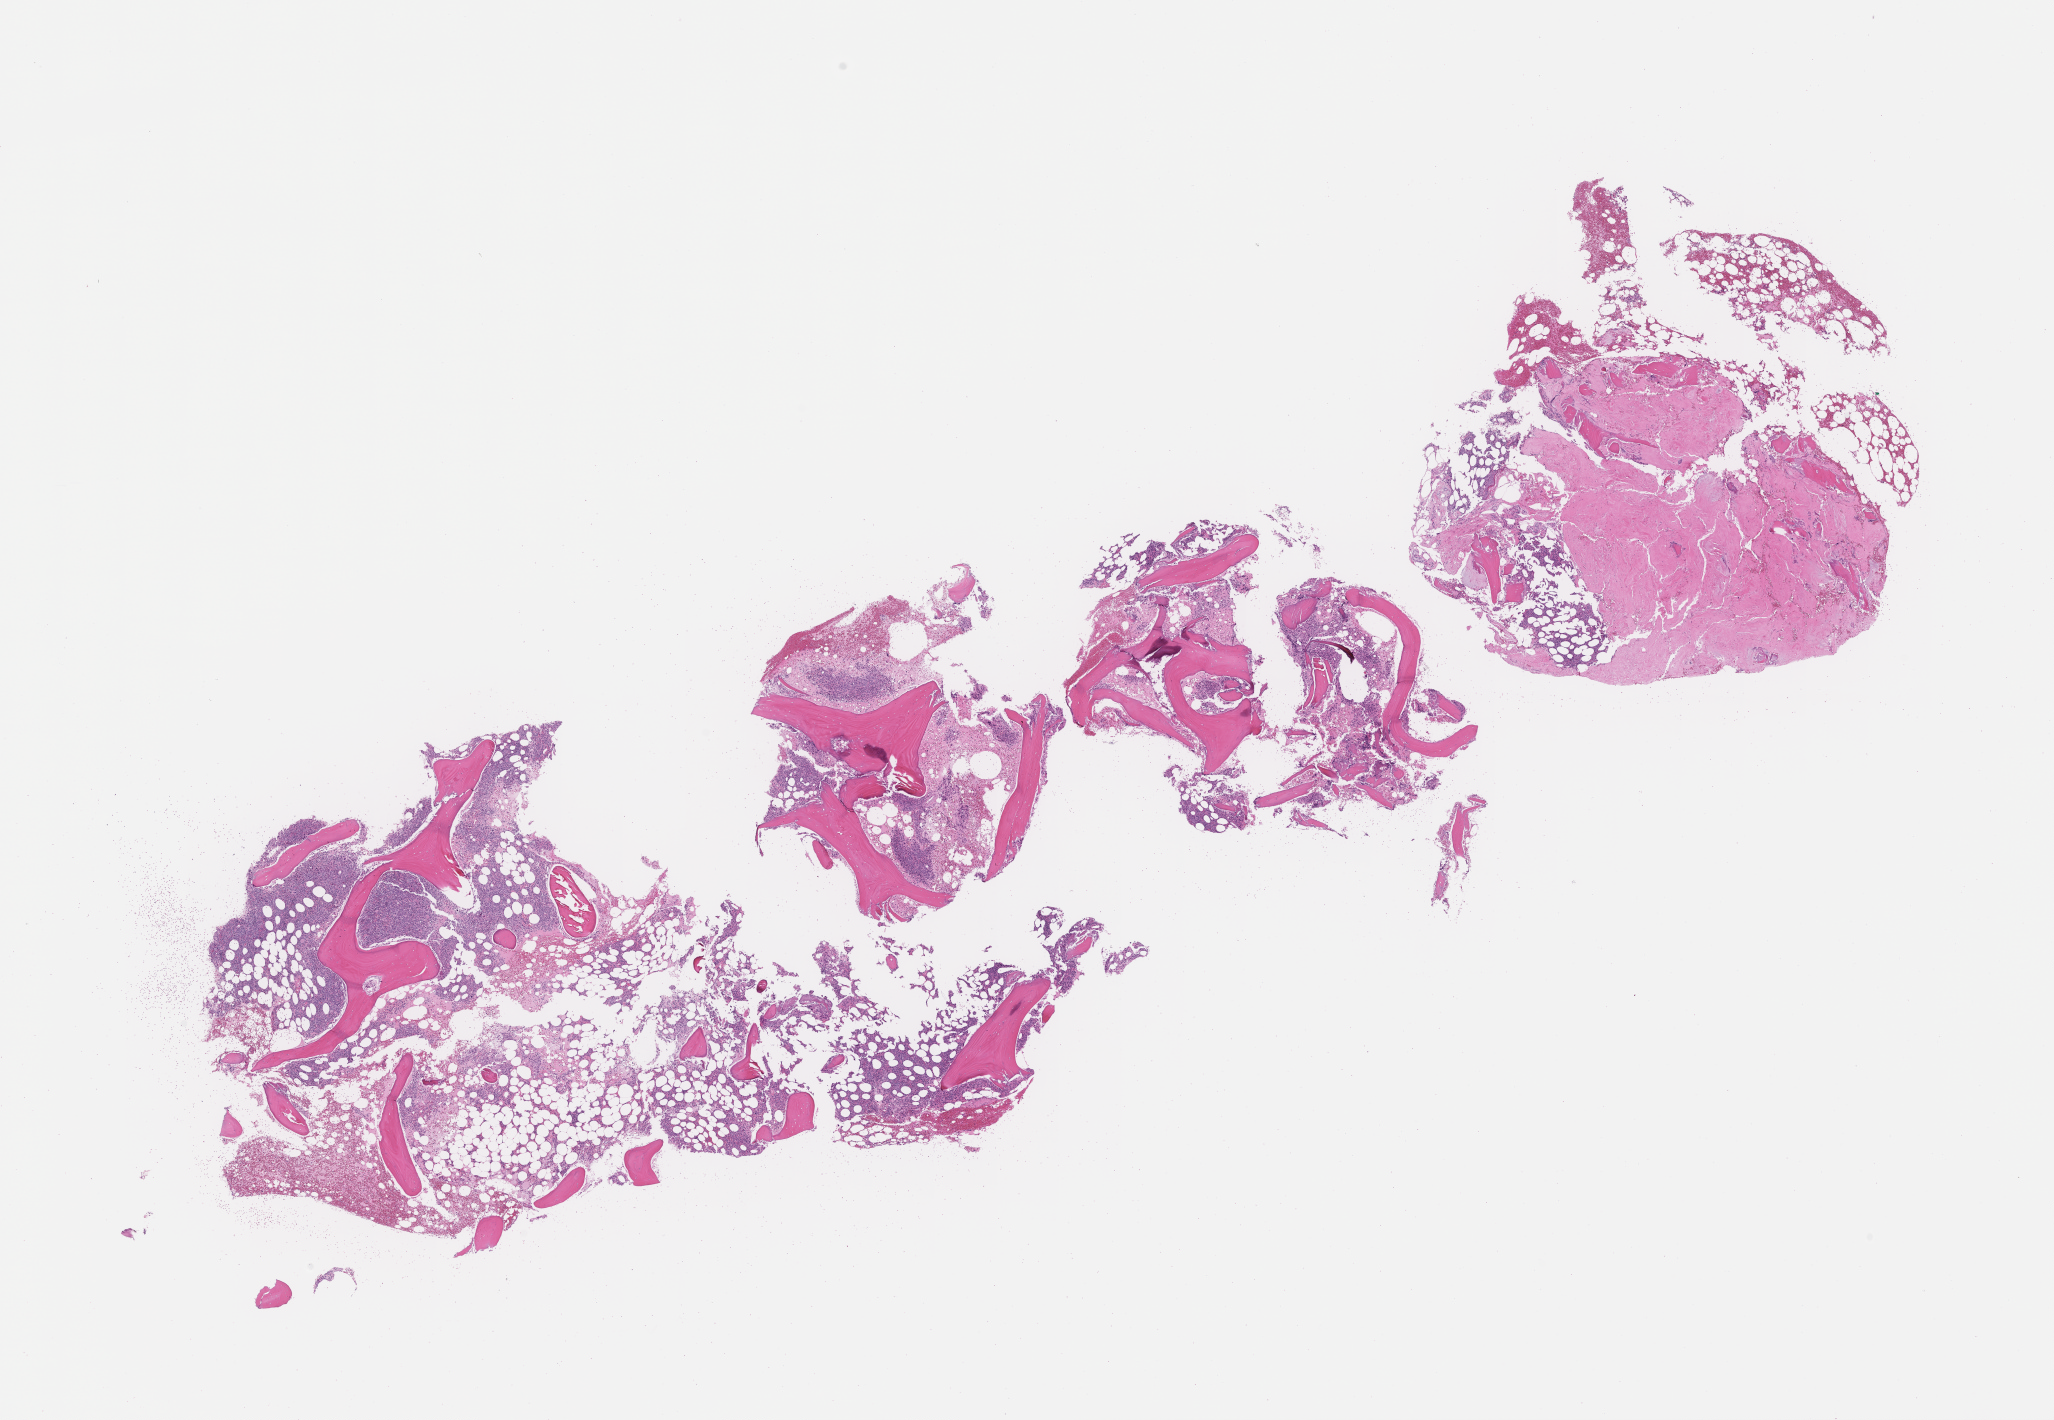
Digitized H&E-stained section — a low-resolution overview of the entire scanned area, about 16.6 x 11.5 mm, FFPE section, tissue site: bone marrow, archival tissue. Female patient.
- this section: primary tumour tissue
- diagnosis: Plasma Cell Myeloma